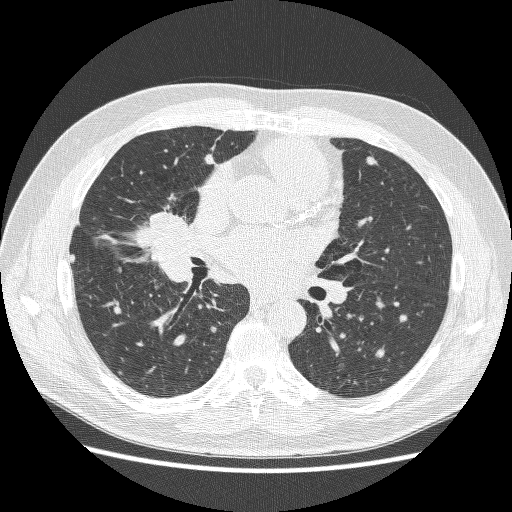
Chest CT (low-dose screening protocol), one axial image, first (baseline) screen, lung window (W 1500 / L -600 HU), lung (sharp) reconstruction kernel (BONE), slice 143 of 251 in the series, 512 × 512 image matrix, field of view 360 × 360 mm. Male participant, aged 59 years at enrolment. Former smoker at enrolment.
Expert-annotated lung lesion, box from (x=125, y=198) to (x=198, y=267) px. Screening reader's record for this exam: no non-calcified nodule ≥4 mm recorded. Official screen result: positive, change unspecified: nodule(s) >= 4 mm or enlarging nodule(s), mass(es), or other non-specific abnormalities suspicious for lung cancer. Later outcome: lung cancer diagnosed 24 days after this screen — adenocarcinoma, NOS, right middle lobe, poorly differentiated (G3), stage IV (AJCC 6th edition), 54 mm at pathology.